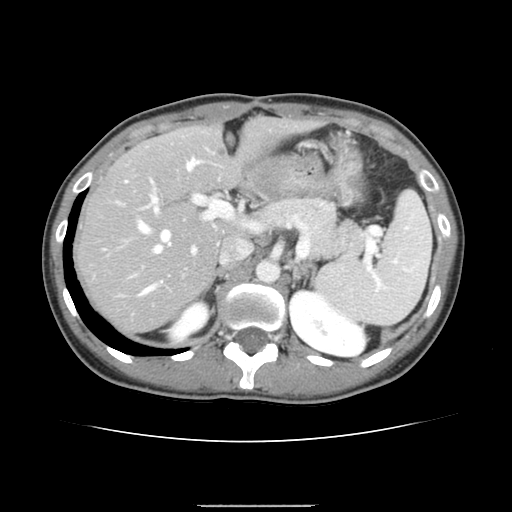
Contrast-enhanced abdominal CT, one axial slice. Slice 97 of 150 in the series (ordered by position). Intravenous contrast given. Soft-tissue window (W 400 / L 40 HU). 2.5 mm slice thickness. 512 × 512 image matrix. Female patient, age 32 years. Case-level facts recorded for this patient, not image findings: diagnosis: colorectal cancer liver metastases, imaged before liver resection; multiple liver metastases: yes; largest metastasis: 0.7 cm; disease in both lobes: no.
Structures marked on this image (manually delineated by an expert):
- hepatic veins: bounding box <138,158,200,294> (left, top, right, bottom; pixels)
- liver: <77,121,307,332>
- planned liver remnant (the part of the liver to remain after resection): <77,121,307,281>
- portal vein (with intrahepatic branches): <125,179,232,282>